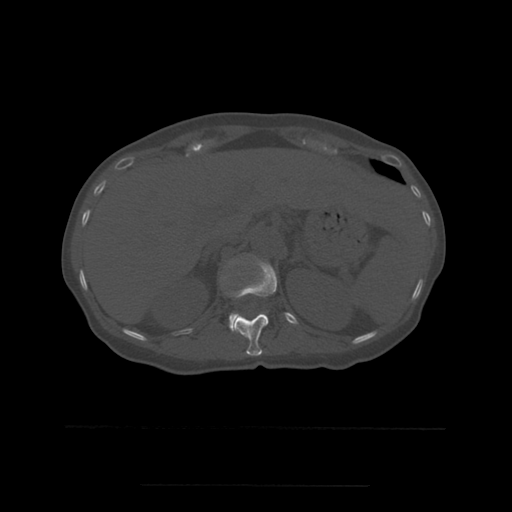
CT including the spine, one axial slice; position 251 of 544 along the scan axis; bone window (W 1800 / L 400 HU); 1.25 mm slice thickness; 512 × 512 image matrix. Patient age 58 years. Case-level facts recorded for this patient, not image findings: primary cancer: lung.
Structures marked on this image (semi-automatically segmented with operator editing):
- L1 vertebra: bounding box [x1, y1, x2, y2] px = [229, 314, 239, 332]
- T12 vertebra: [231, 259, 278, 356]